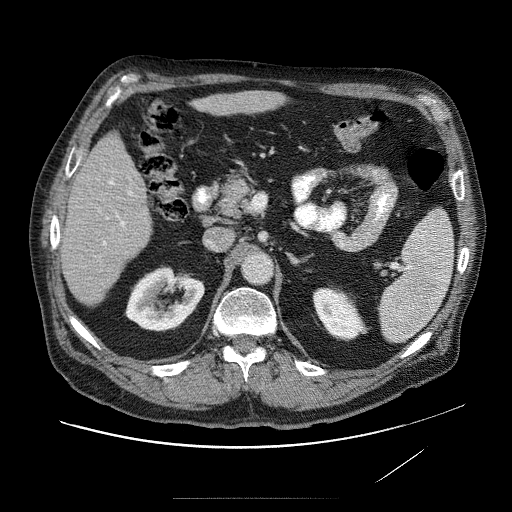
Contrast-enhanced abdominal CT (liver protocol), one axial slice. Slice 31 of 89 in the series (ordered by position). 120 kVp. Soft-tissue window (W 400 / L 40 HU). 2.5 mm slice thickness. 512 × 512 image matrix. From the clinical record (not read from this slice): diagnosis: hepatocellular carcinoma (patient treated with transarterial chemoembolisation; whether this scan precedes or follows treatment is not stated here); TNM stage (as recorded): Stage-IVA; Child-Pugh class: A; tumour differentiation: moderately differentiated.
Annotated regions visible in this slice (semi-automatic segmentation, software-assisted and operator-edited):
- liver parenchyma outside the tumour (the mass and vessels are separate outlines, so this box may not span the whole liver): box from (x=62, y=86) to (x=298, y=310) px
- liver vessels: (x=98, y=105)–(x=200, y=285)